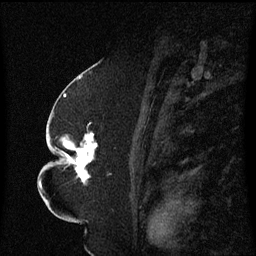
Breast MRI (dynamic contrast-enhanced), one sagittal slice. Position 35 of 60 along the scan axis. Dynamic contrast-enhanced series, image 2 of 3 at this slice position (ordered by acquisition). 1.5 T. TE 4.2 ms, TR 8.4 ms. 2.3 mm slice thickness. 256 × 256 image matrix. Patient: female, 52 years. Case-level facts recorded for this patient, not image findings: setting: breast cancer imaged before/during neoadjuvant chemotherapy; receptor status: HR-positive, HER2-negative.
Outlined on this slice (semi-automatic segmentation, software-assisted and operator-edited):
- analysis volume of interest (the breast-tissue region the enhancement analysis was run in; not a lesion): box from (x=49, y=124) to (x=111, y=185) px
- tumour enhancement mask (voxels above the 70 % enhancement threshold inside the analysis volume of interest): (x=60, y=134)–(x=98, y=185)